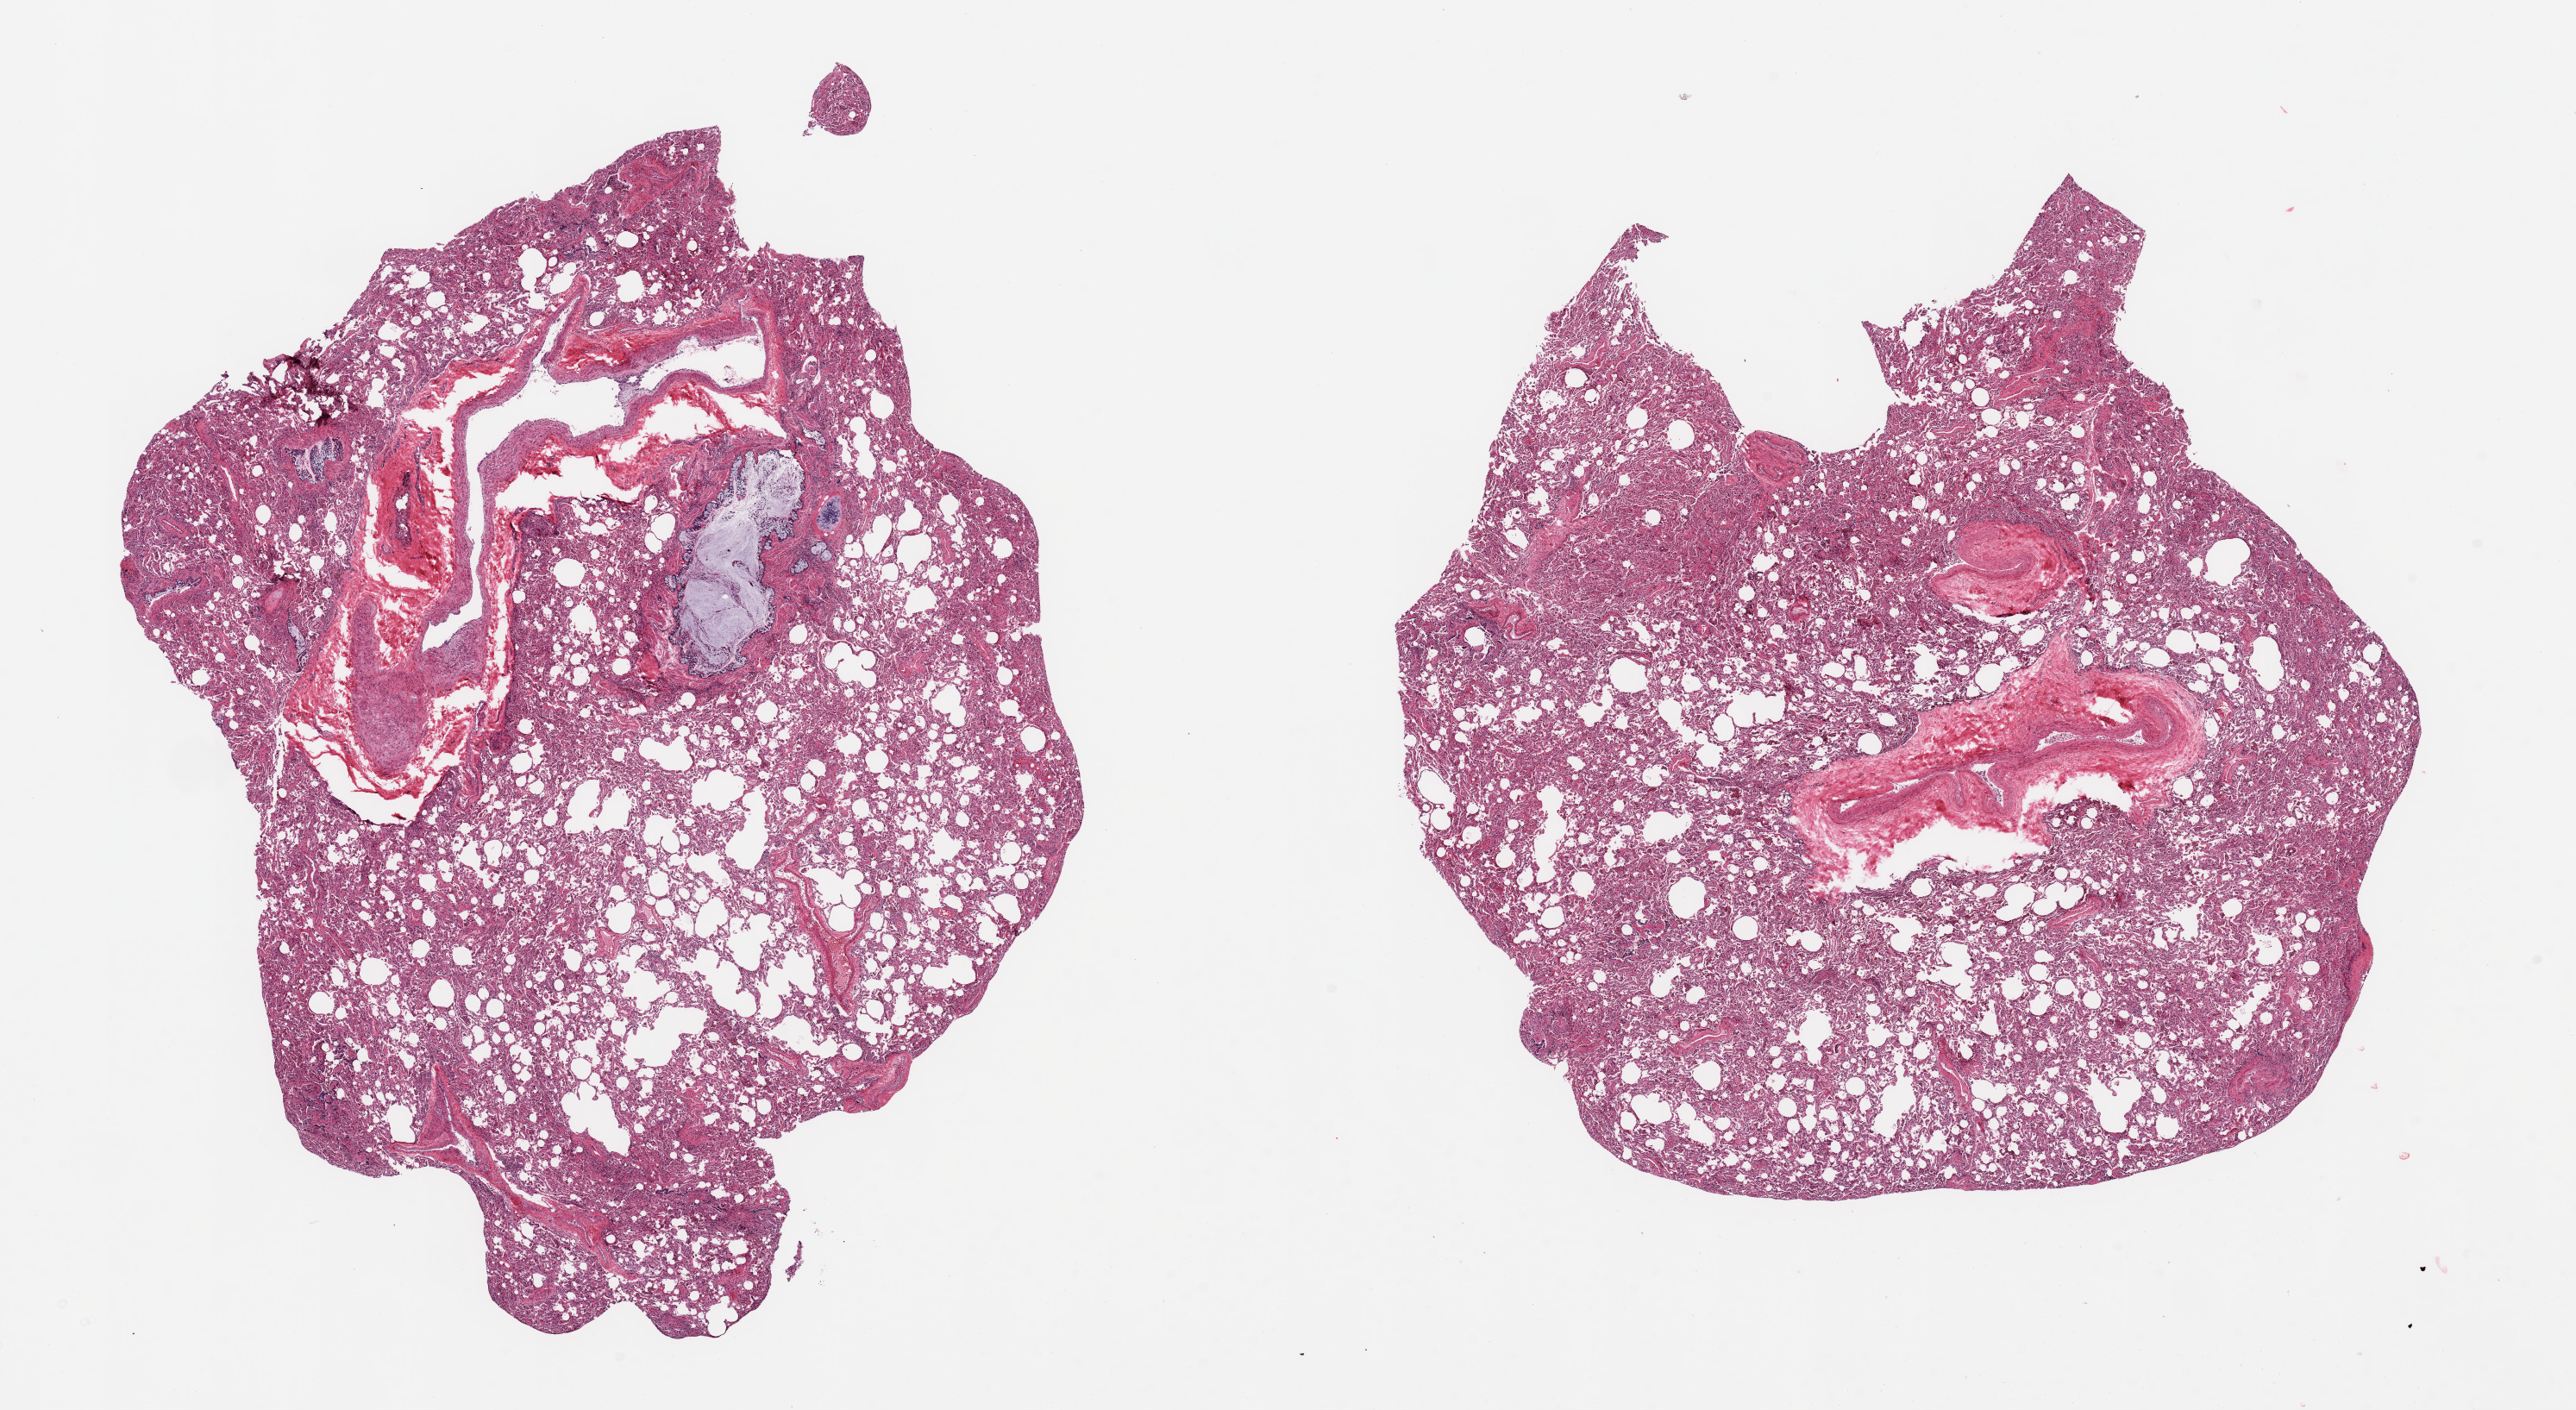
Digitized hematoxylin and eosin (H&E)-stained section — shown as a low-resolution overview of the whole scanned area (about 23.6 x 12.9 mm, slide scanned at 20x); PAXgene-fixed, paraffin-embedded tissue; section of lung (target tissue); donor tissue sample. Donor: female.
• pathologist's review note for this sample: 2 pieces; collapsed alveolar spaces and congestion; bronchus and bronchioles filled with mucus; larger vessels